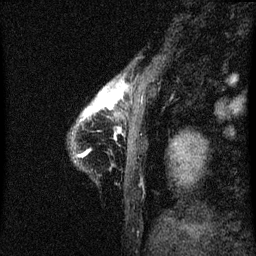
Breast MRI (dynamic contrast-enhanced), one sagittal slice; position 6 of 60 along the scan axis; dynamic contrast-enhanced series, image 2 of 3 at this slice position (ordered by acquisition); 1.5 T; TE 4.2 ms, TR 8 ms; 2 mm slice thickness; 256 × 256 image matrix, field of view 180 × 180 mm. Patient: female, 38 years.
Outlined on this slice (semi-automatic segmentation, software-assisted and operator-edited):
- analysis volume of interest (the breast-tissue region the enhancement analysis was run in; not a lesion): box from (x=76, y=82) to (x=122, y=133) px
- tumour enhancement mask (voxels above the 70 % enhancement threshold inside the analysis volume of interest): (x=87, y=82)–(x=122, y=115)